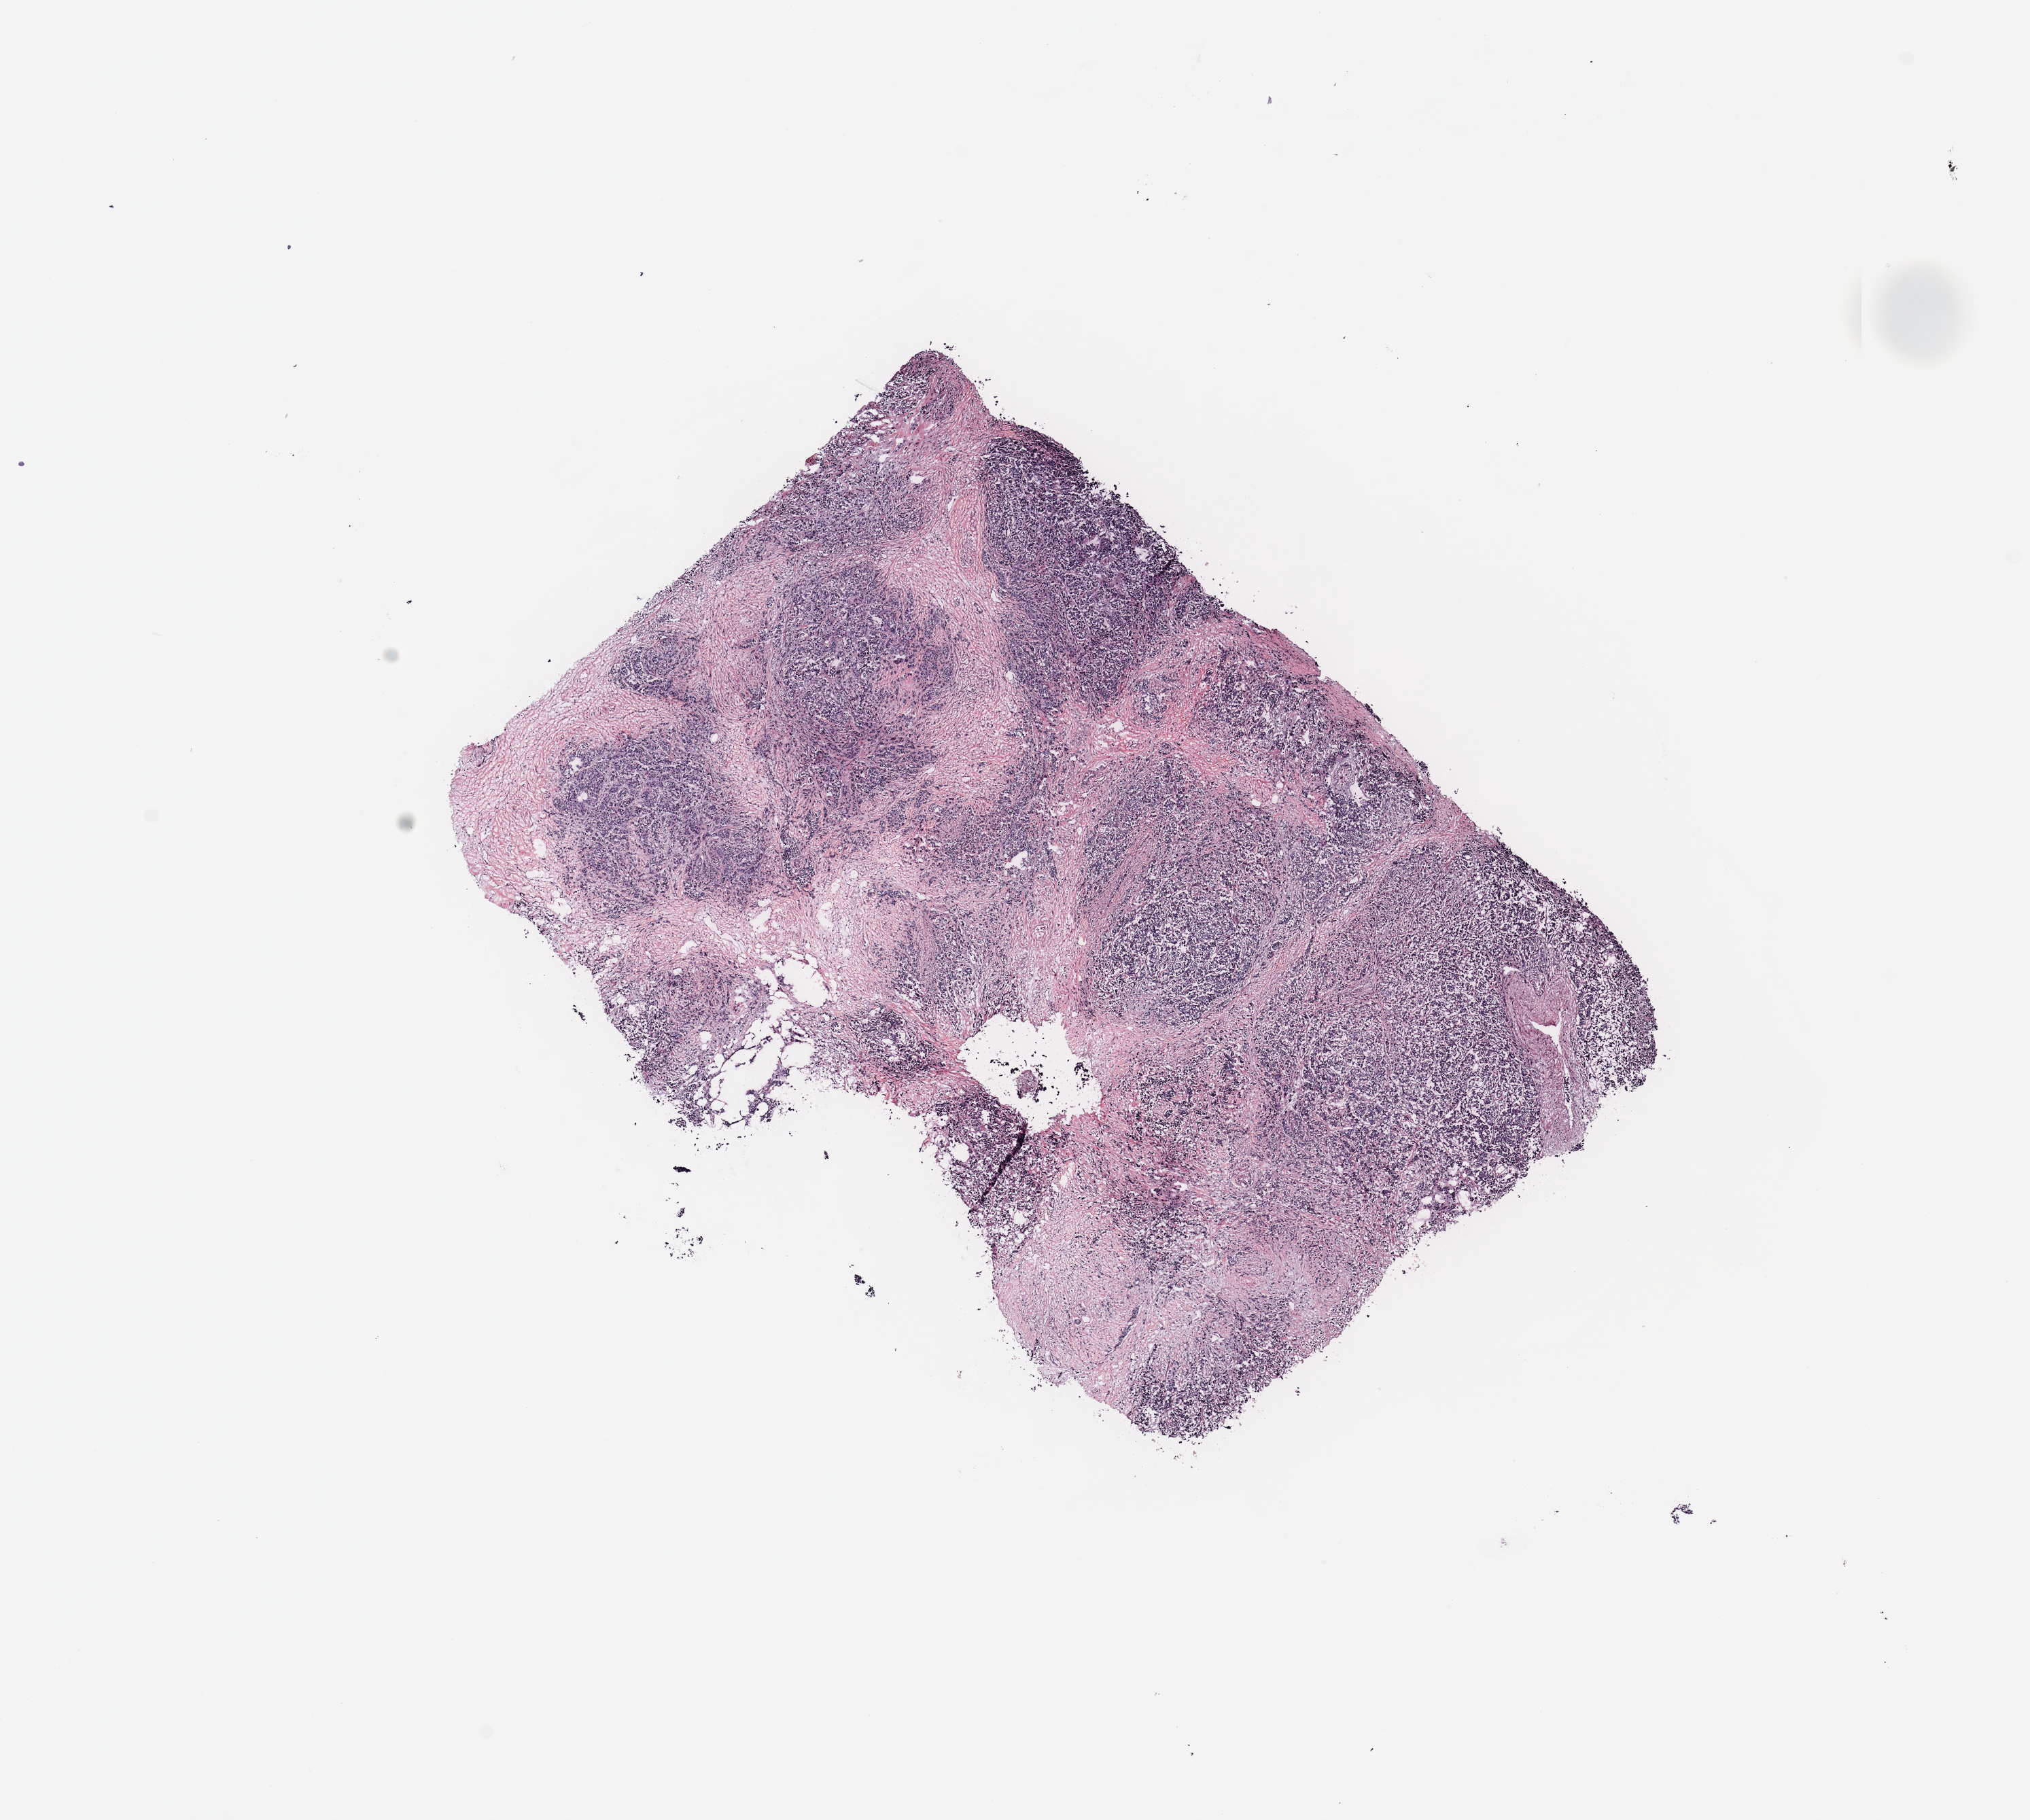
Hematoxylin and eosin (H&E) stained whole-slide image — a low-resolution overview of the entire scanned area, about 11.8 x 10.6 mm (slide scanned at 20x).
Specimen: breast, tissue type not recorded.